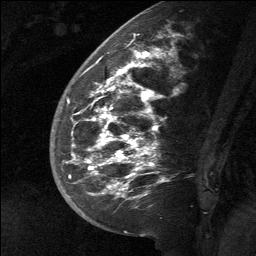
Breast MRI (dynamic contrast-enhanced), one sagittal slice; slice 25 of 64 in the series (ordered by position); dynamic contrast-enhanced study with each time point stored as its own series, time point 2 of 3 at this slice position (early post-contrast, ordered by acquisition time); 1.5 T; TE 4.8 ms, TR 27 ms; 2 mm slice thickness; 256 × 256 image matrix, field of view 180 × 180 mm. Patient: female, 39 years. From the clinical record (not read from this slice): setting: breast cancer imaged before/during neoadjuvant chemotherapy; receptor status: HER2-positive.
Annotated regions visible in this slice (semi-automatically segmented with operator editing):
- analysis volume of interest (the breast-tissue region the enhancement analysis was run in; not a lesion): bounding box <58,40,174,217> (left, top, right, bottom; pixels)
- tumour enhancement mask (voxels above the 90 % enhancement threshold inside the analysis volume of interest): <68,50,163,198>